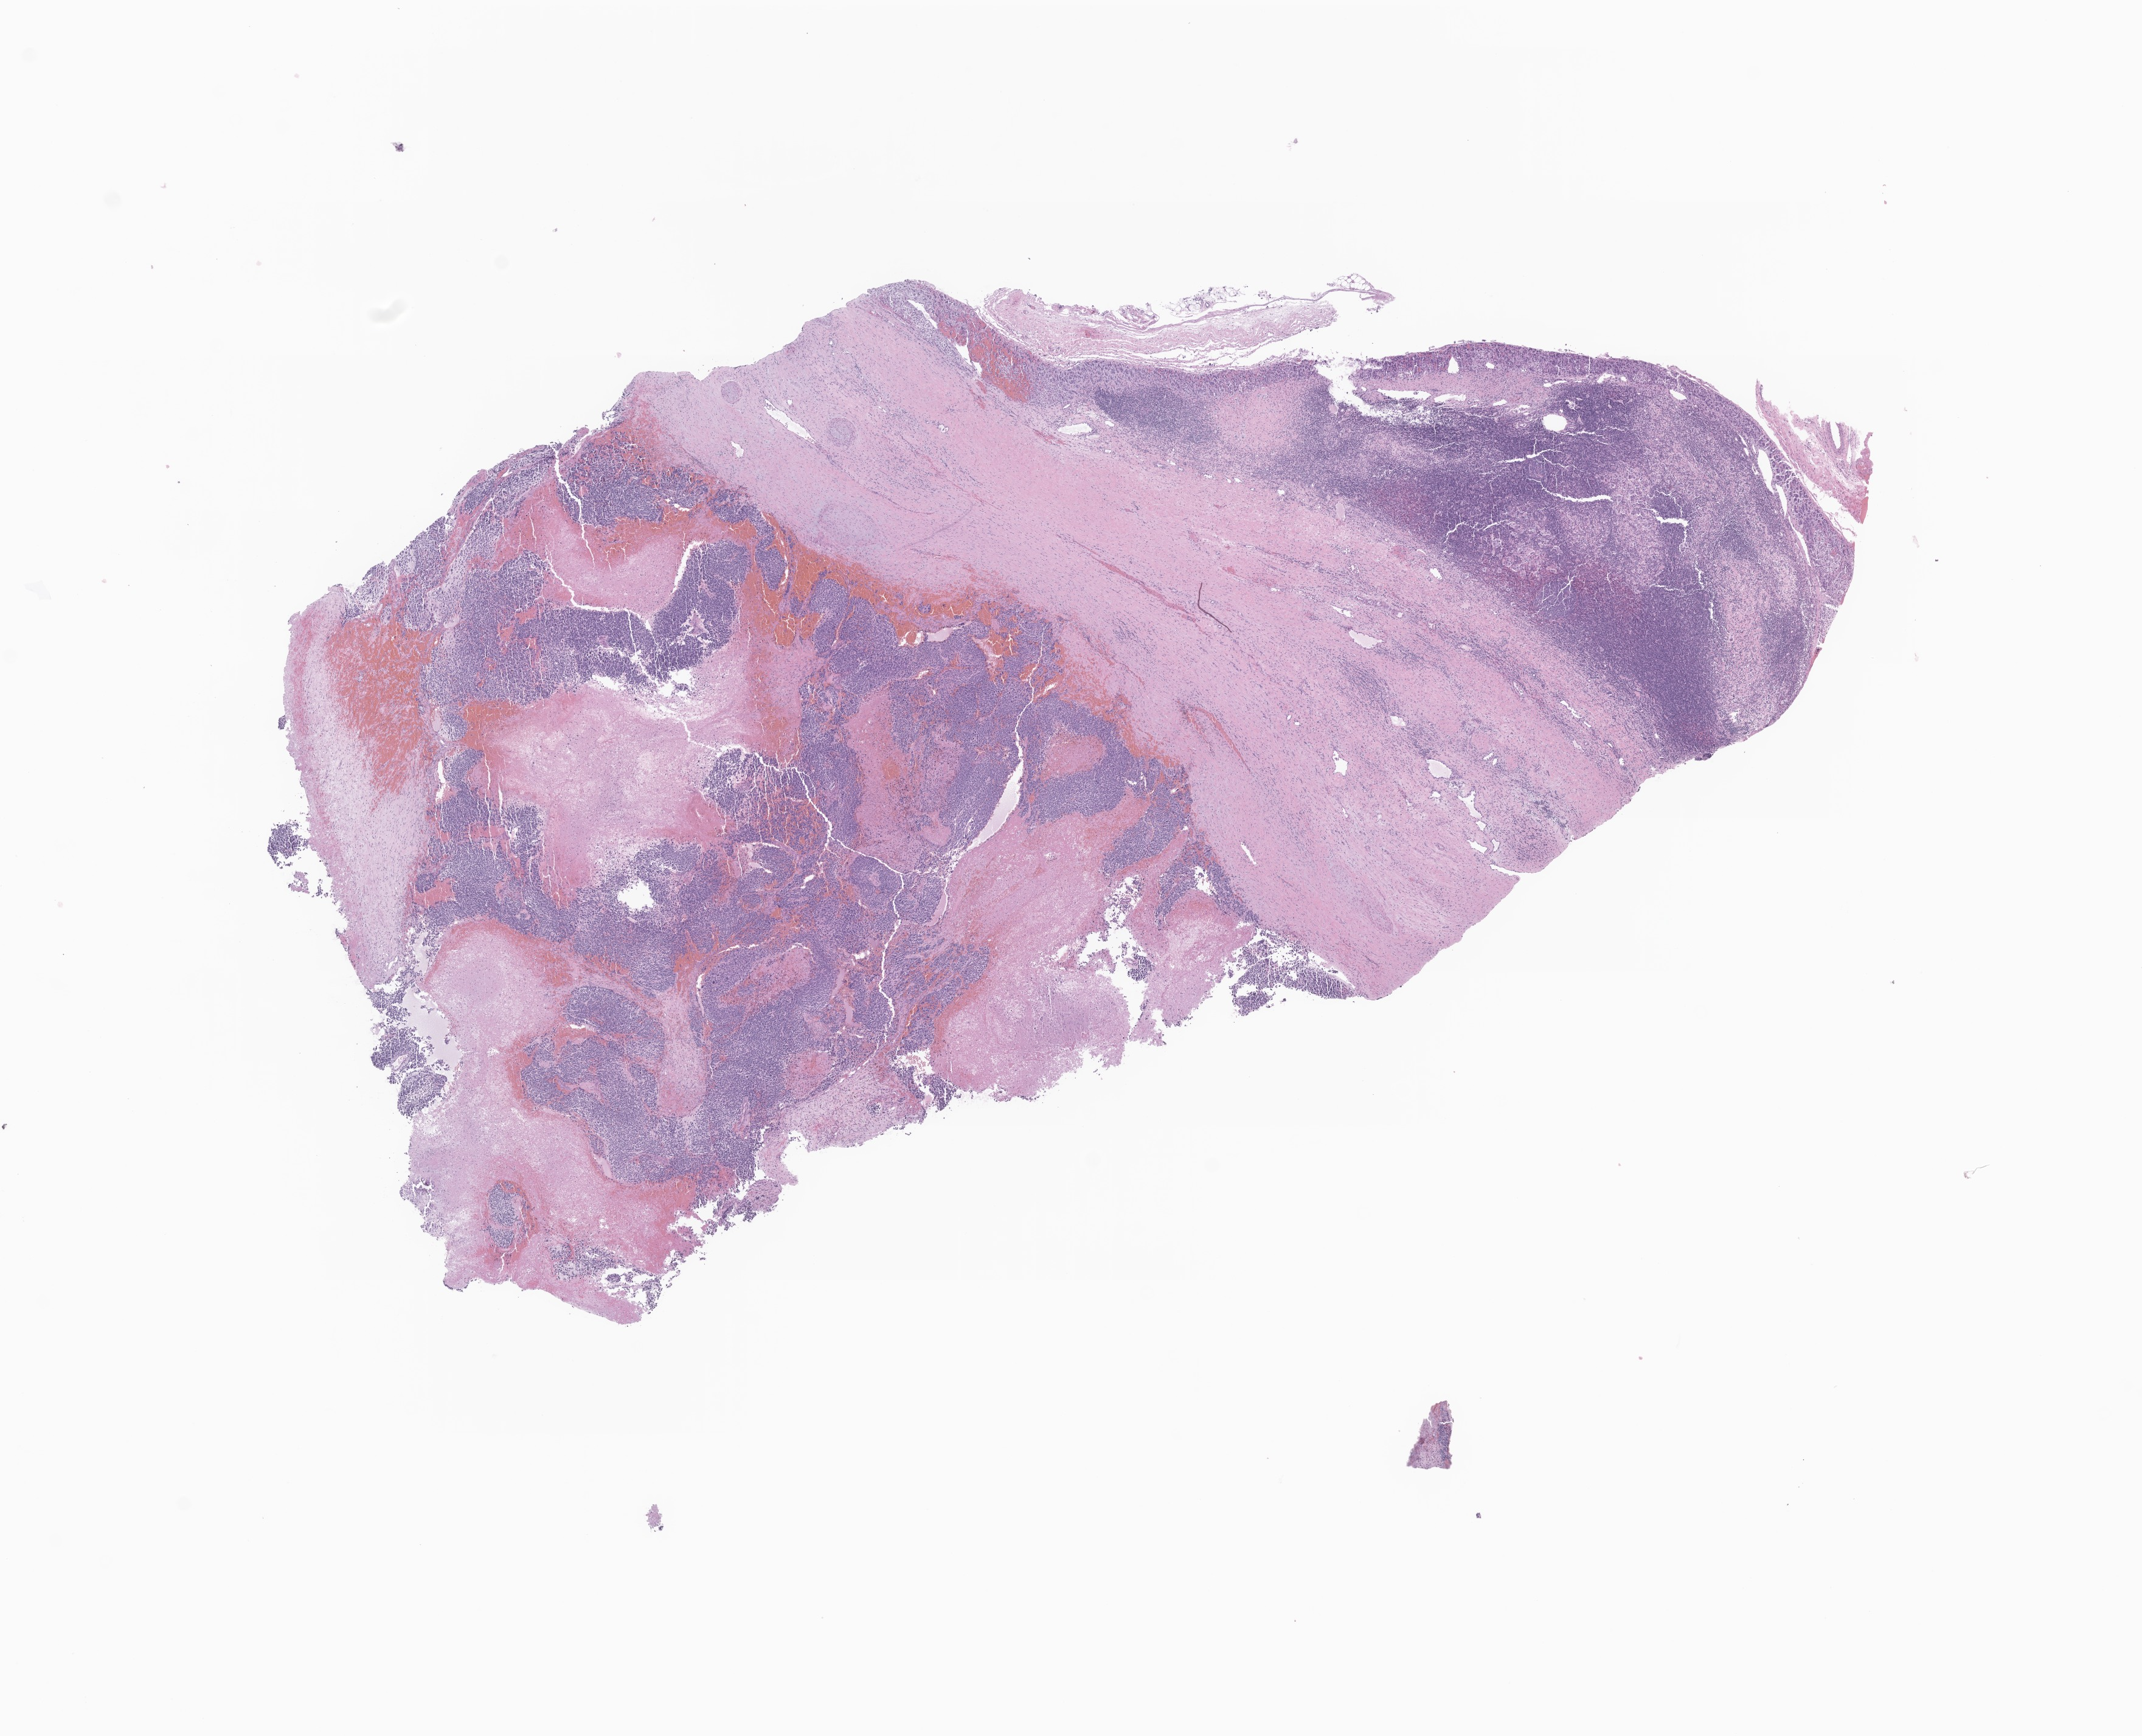
Digitized hematoxylin and eosin (H&E)-stained section of tumor tissue from the adrenal gland — shown as a low-resolution overview of the whole scanned area (about 14.8 x 12.0 mm), formalin-fixed, paraffin-embedded (FFPE) tissue. Patient: male, age 39 months (3 years 3 months).
Recorded diagnosis: Neuroblastoma, NOS.